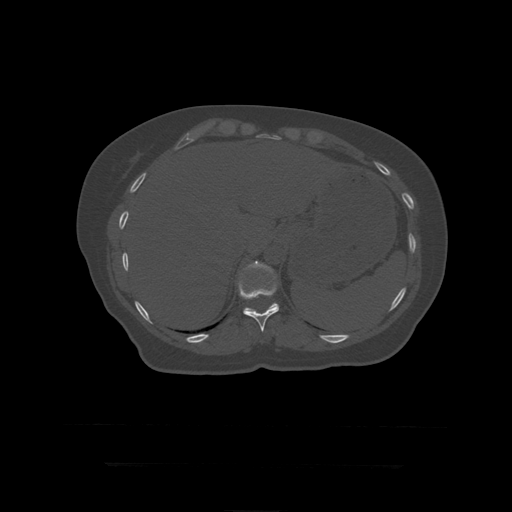
CT including the spine, one axial slice; slice 214 of 399 in the series (ordered by position); bone window (W 1800 / L 400 HU); 1.25 mm slice thickness; 512 × 512 image matrix. Patient age 41 years. Case-level facts recorded for this patient, not image findings: primary cancer: breast.
Annotated regions visible in this slice (semi-automatic segmentation, software-assisted and operator-edited):
- T11 vertebra: bounding box [x1, y1, x2, y2] px = [238, 265, 279, 332]
- T12 vertebra: [243, 261, 279, 312]